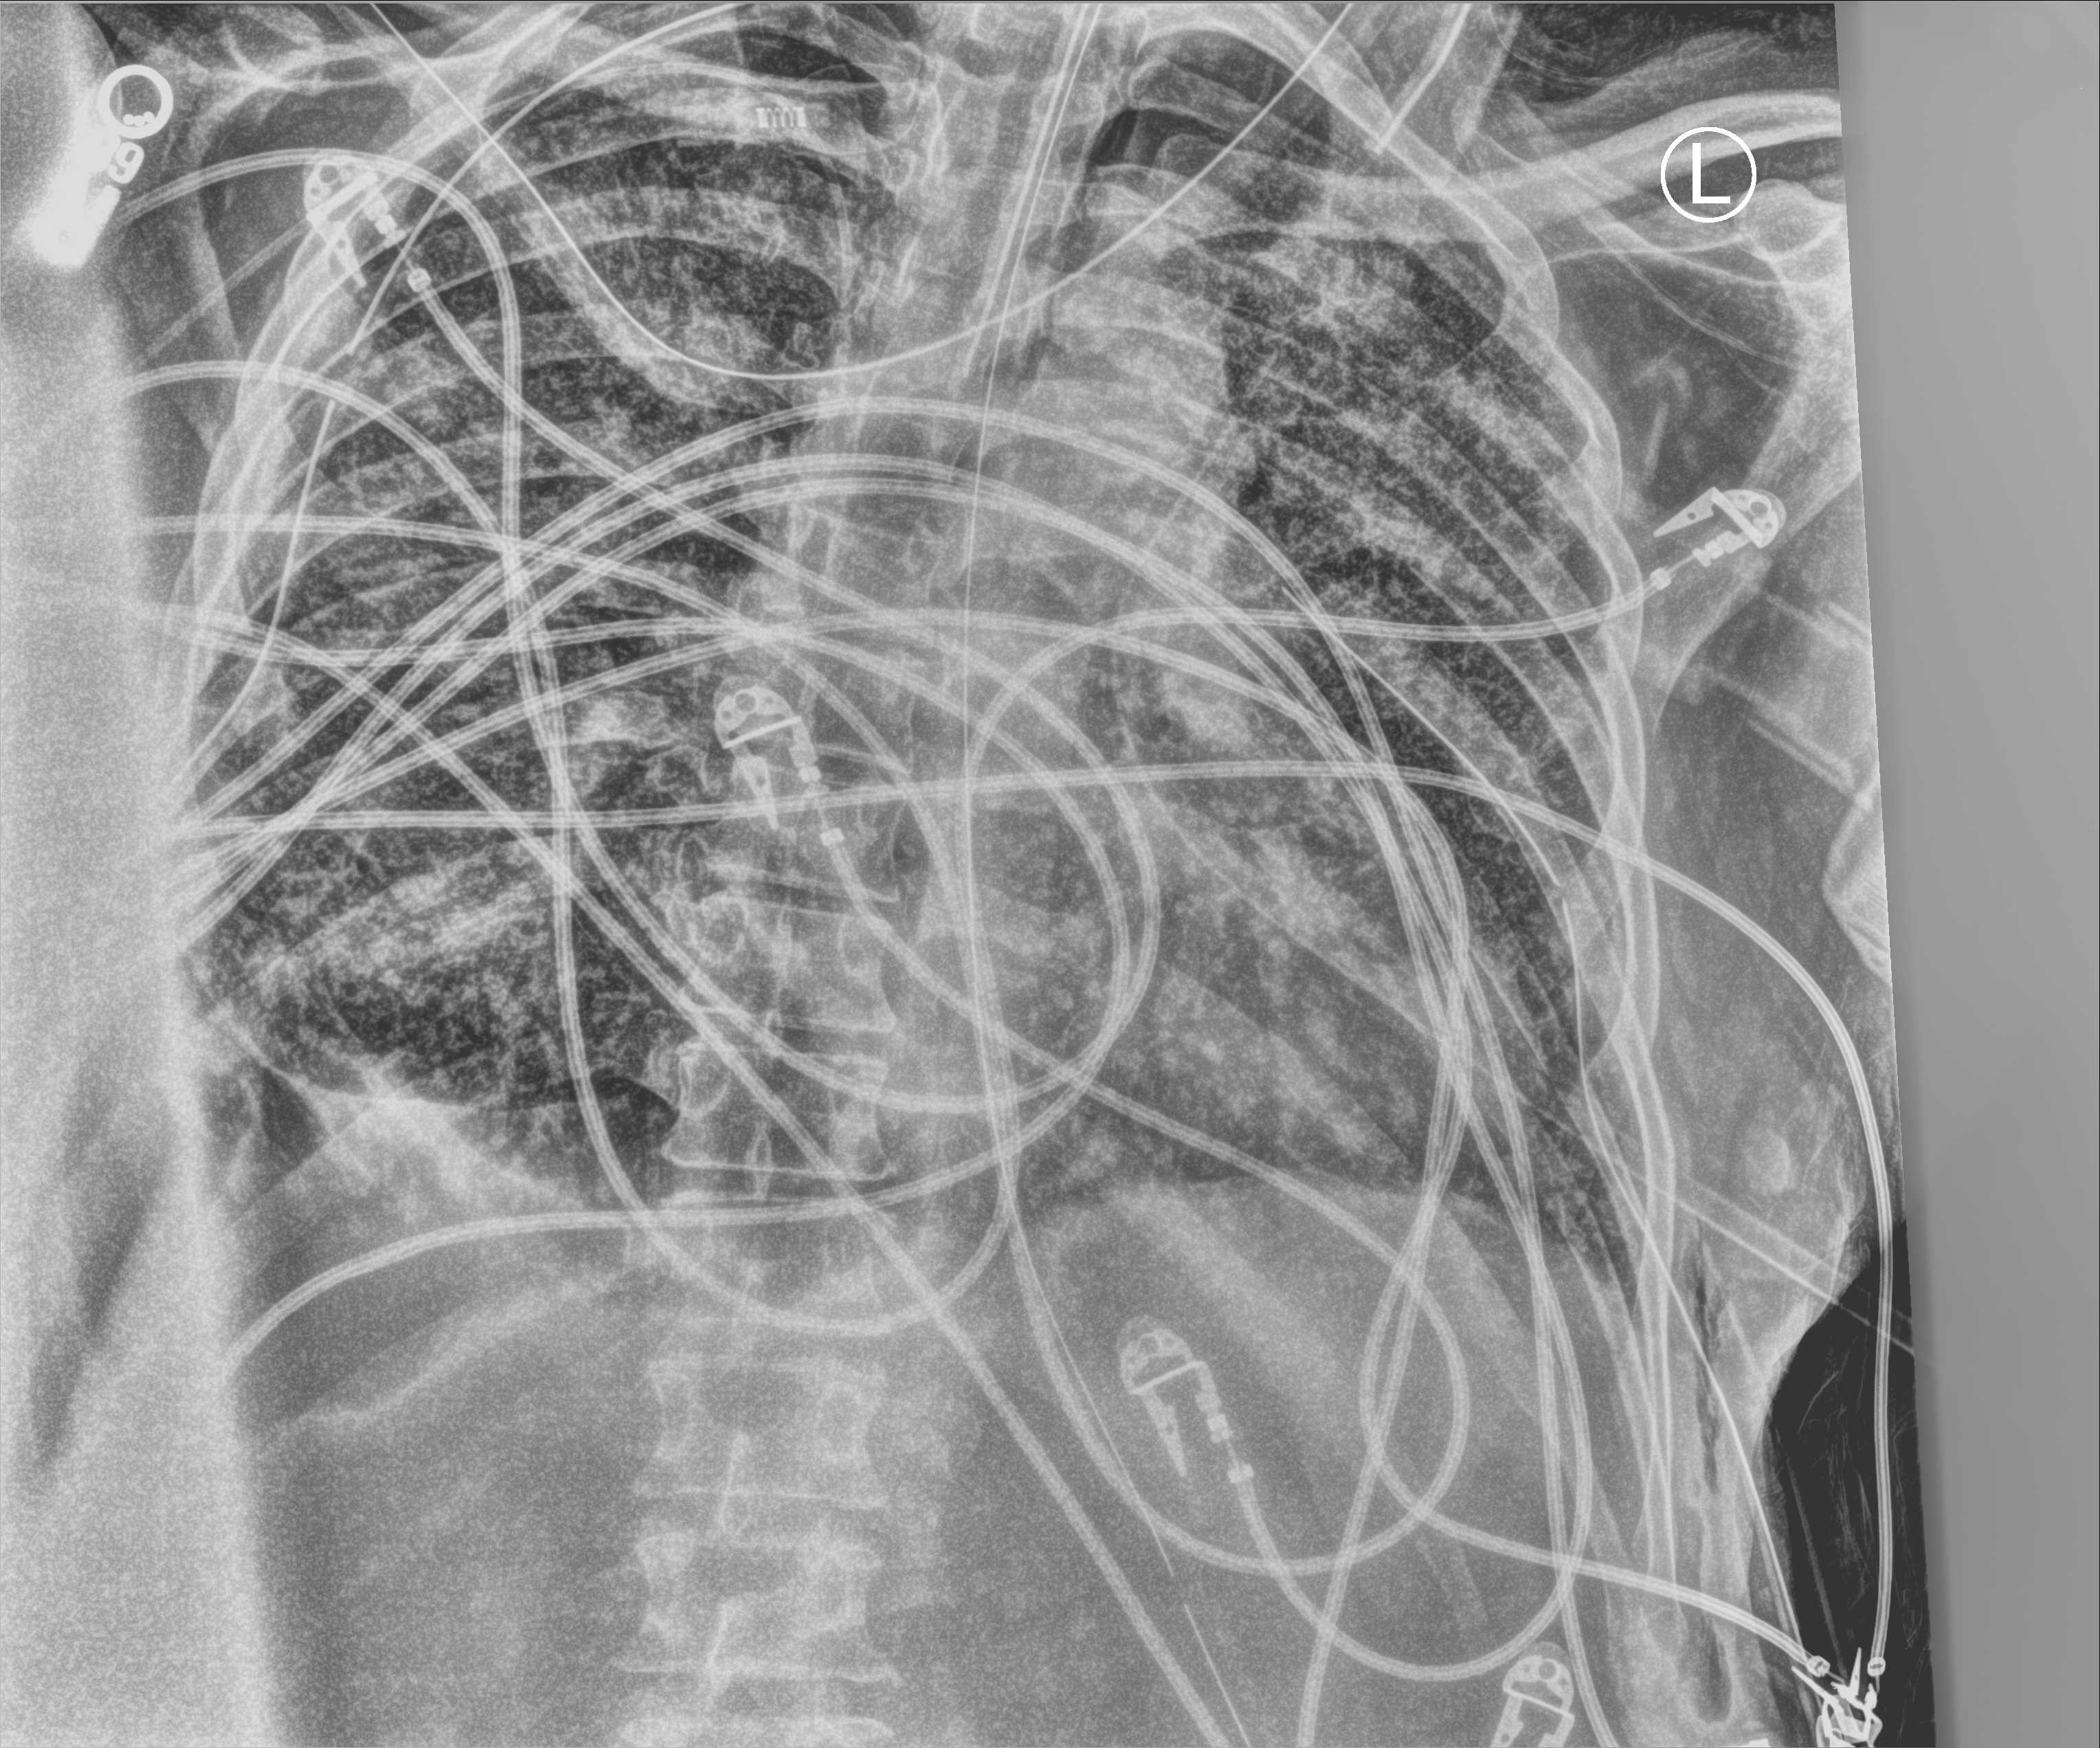
Portable chest radiograph, anteroposterior (AP) projection. Male patient hospitalised with COVID-19, age 60–74 years.
Admission-level facts for this patient (not findings on this image; timing relative to this image not recorded):
- hypertension (admission record): no
- COPD (admission record): no